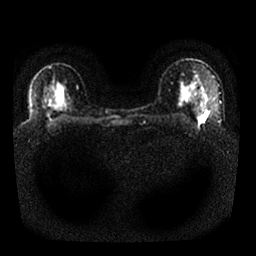
Breast MRI, one axial slice. Slice 17 of 25 in the series (ordered by position). Diffusion-weighted series; image 2 of 4 stored at this slice position (different b-values; order by instance number). 1.5 T. 256 × 256 image matrix, field of view 330 × 330 mm. Female patient.
Outlined on this slice (outlined manually by an expert reader):
- tumour on diffusion-weighted imaging: box from (x=197, y=117) to (x=203, y=123) px